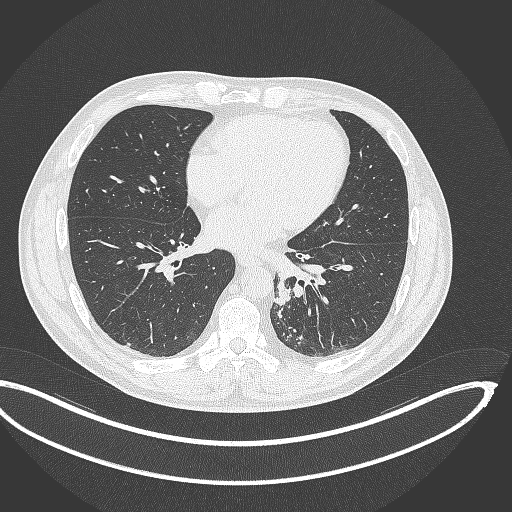
Chest CT, one axial slice. Position 143 of 362 along the scan axis. Reconstruction kernel B70f. 120 kVp. Lung window (W 1500 / L -600 HU). 1 mm slice thickness. 512 × 512 image matrix. Patient: male, 50 years. Case-level facts recorded for this patient, not image findings: clinical TNM (as recorded): T2a N3 M0.
Structures marked on this image (rectangle marked by the reading radiologist):
- lung tumour (recorded histology: squamous cell carcinoma): box from (x=273, y=275) to (x=292, y=307) px